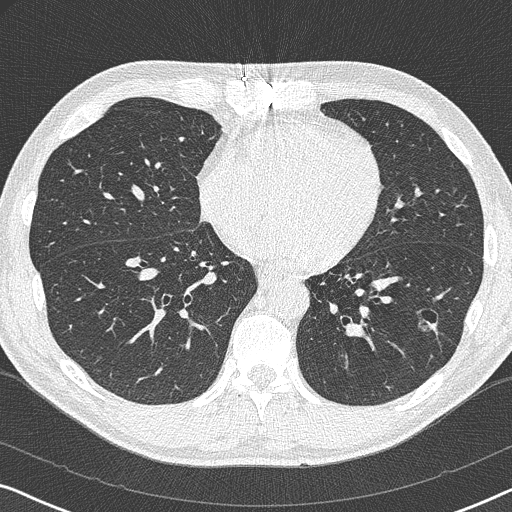
Axial slice from a low-dose chest CT screening exam, first (baseline) screen, lung window (W 1500 / L -600 HU), 1 mm slice thickness, lung (sharp) reconstruction kernel (B50f), 512 × 512 image matrix. Male participant, aged 59 years at enrolment.
Lesion marked by an expert reader, bounding box (x1, y1, x2, y2) in pixels: (409, 303, 449, 336). The screening reader recorded 2 non-calcified nodules or masses ≥4 mm on this exam (left lower lobe, right middle lobe); which of them this box marks is not recorded. Official screen result: positive, change unspecified: nodule(s) >= 4 mm or enlarging nodule(s), mass(es), or other non-specific abnormalities suspicious for lung cancer. Lung cancer was diagnosed 821 days after this screen: adenocarcinoma, NOS, left lower lobe, poorly differentiated (G3), stage IA (AJCC 6th edition), 20 mm at pathology.